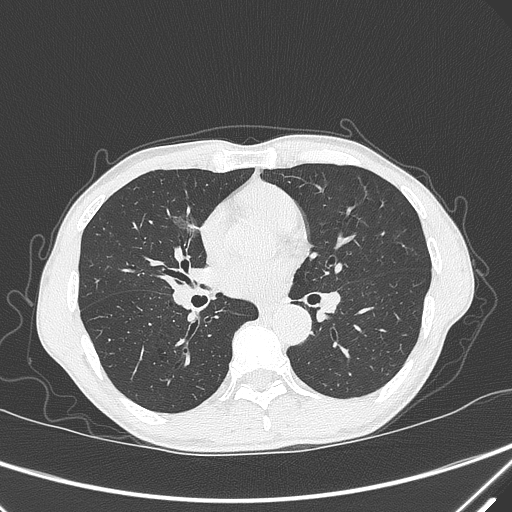
Chest CT, one axial slice. Position 171 of 339 along the scan axis. Lung window (W 1500 / L -600 HU). 512 × 512 image matrix, field of view 350 × 350 mm. Male patient, age 67 years. Case-level facts recorded for this patient, not image findings: clinical TNM (as recorded): T1c N0 M0; histopathological grade: G1-2.
Annotated regions visible in this slice (rectangle marked by the reading radiologist):
- lung tumour (recorded histology: adenocarcinoma): box from (x=168, y=206) to (x=202, y=240) px